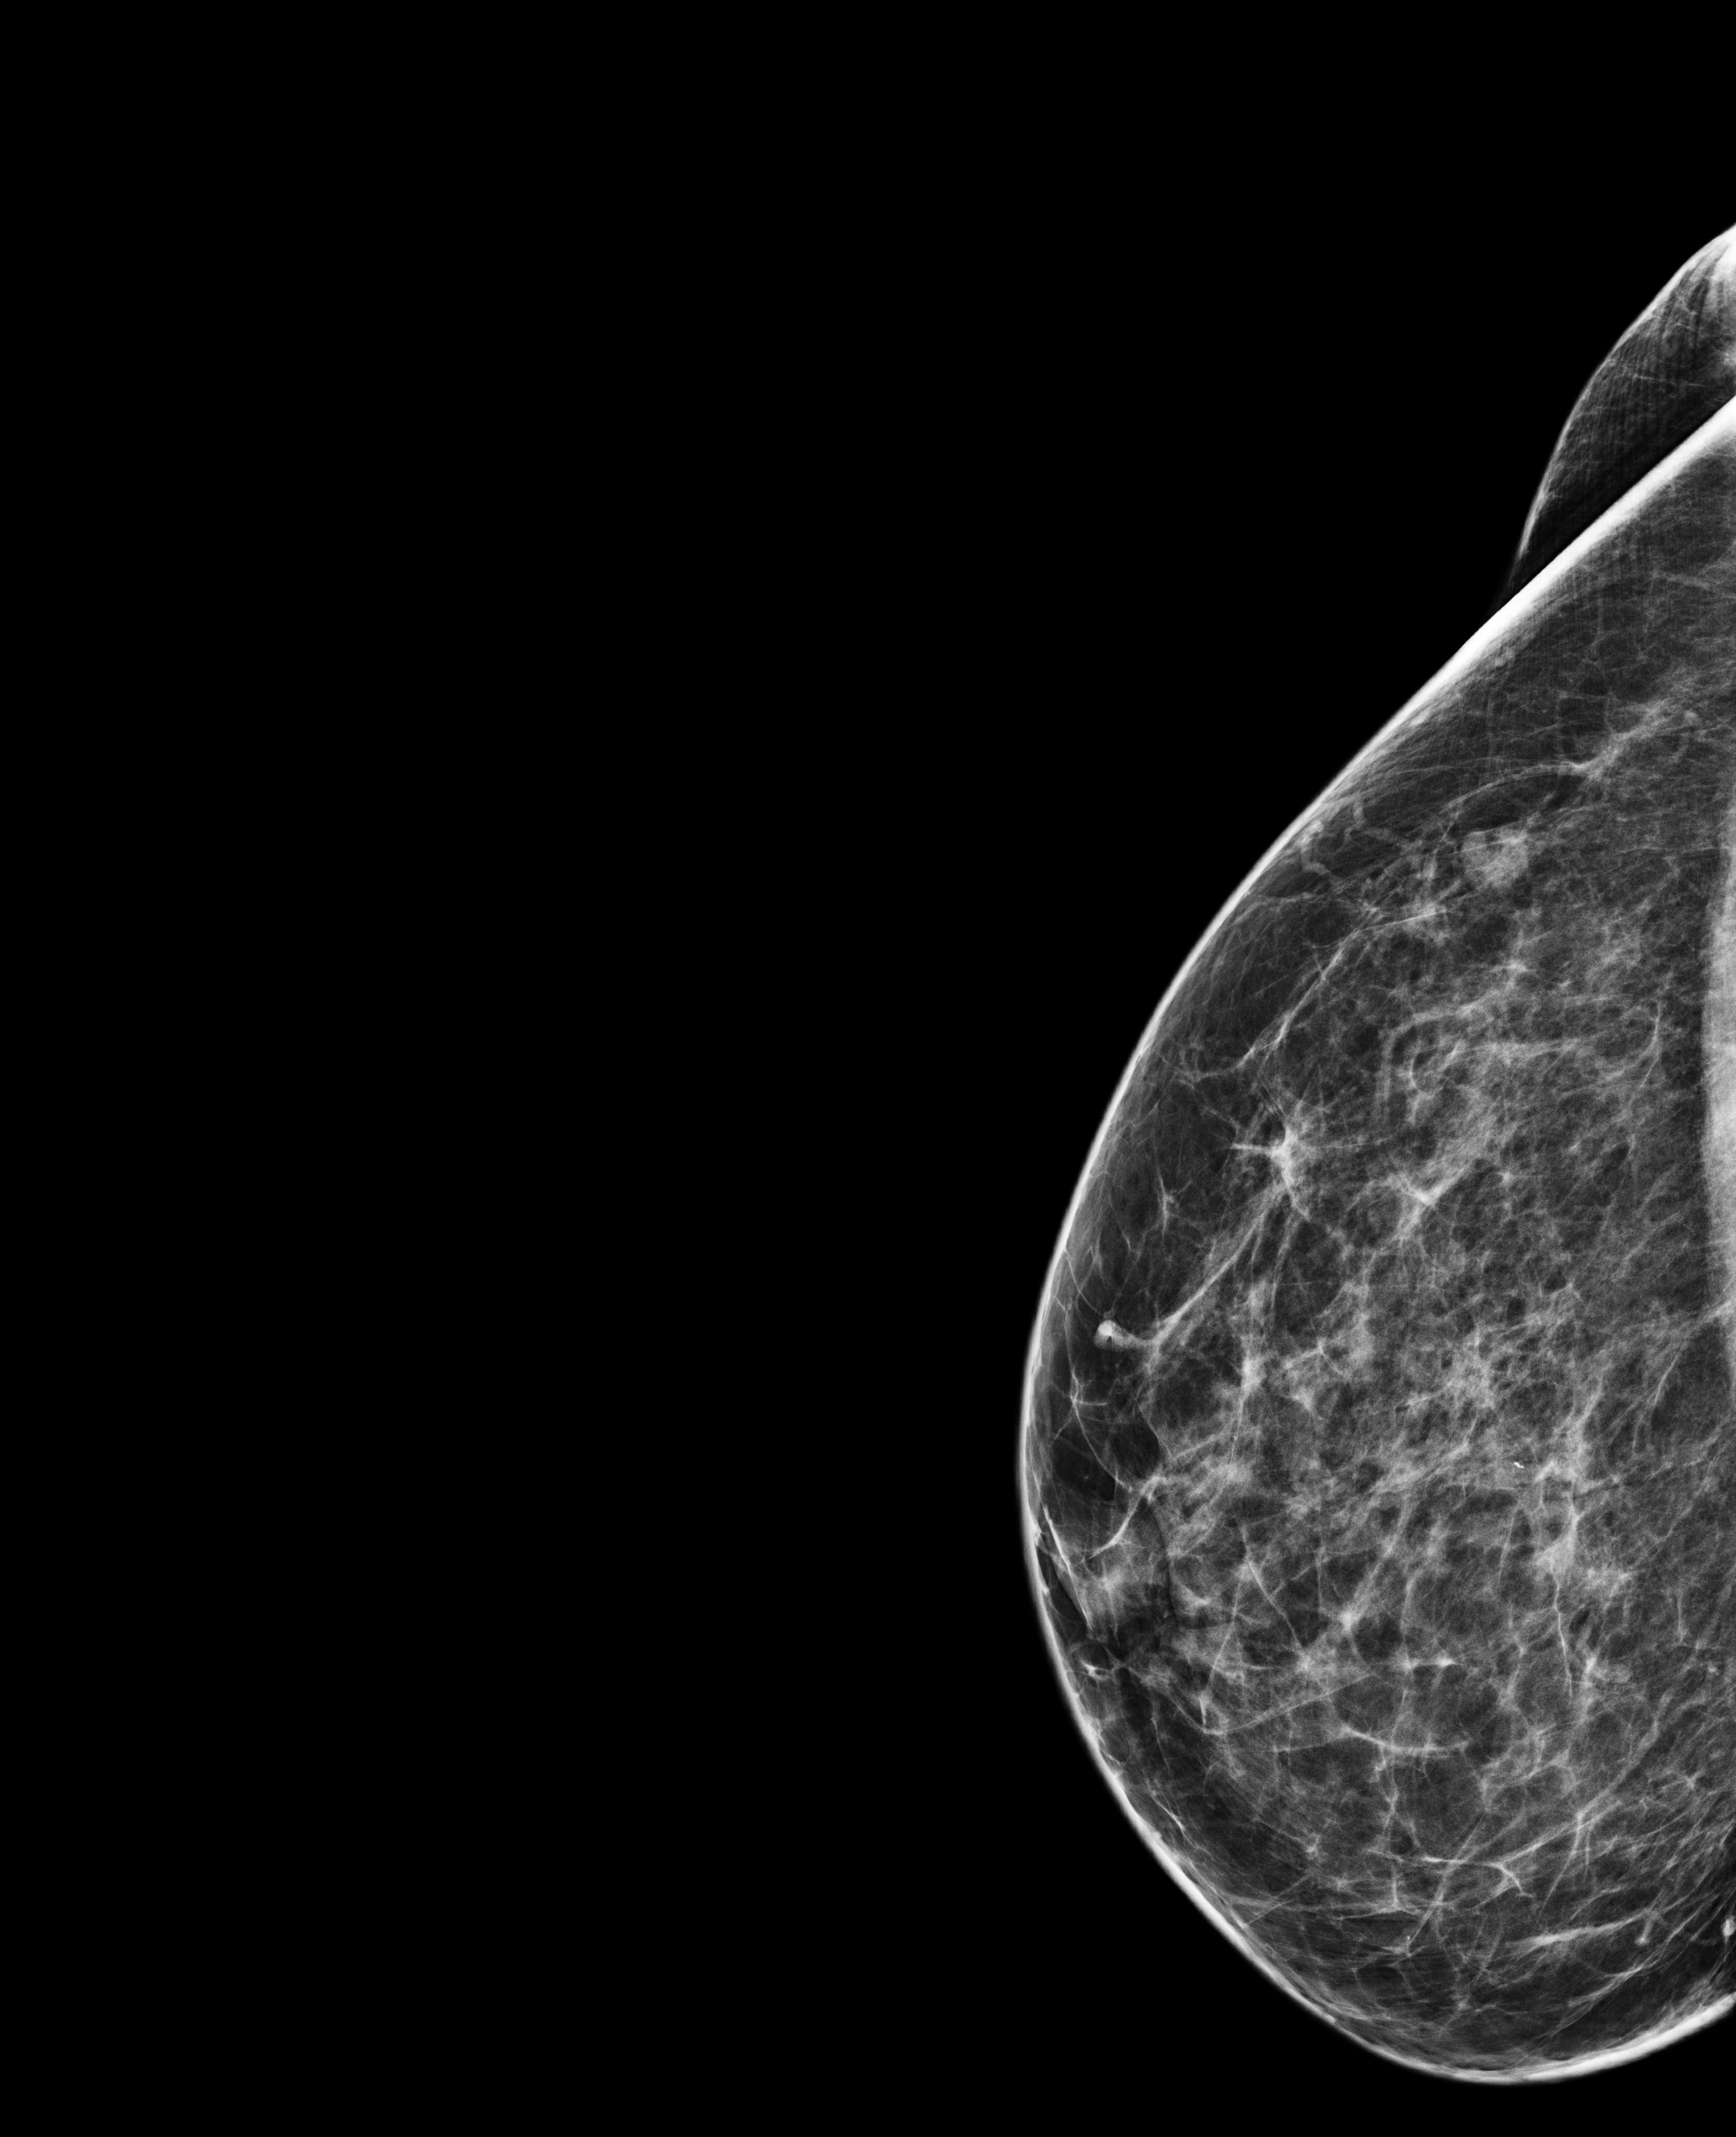
Annual screening mammography examination, compressed breast thickness 56 mm. Patient aged 52 years (female).
Image type: full-field digital mammogram. Breast: right. Projection: exaggerated CC view (lateral). Breast density at the screening exam (both breasts): scattered fibroglandular densities (BI-RADS density category b). Final BI-RADS assessment for this screening round (tomosynthesis exam, both breasts): category 2. Recall: no recall after this screen.